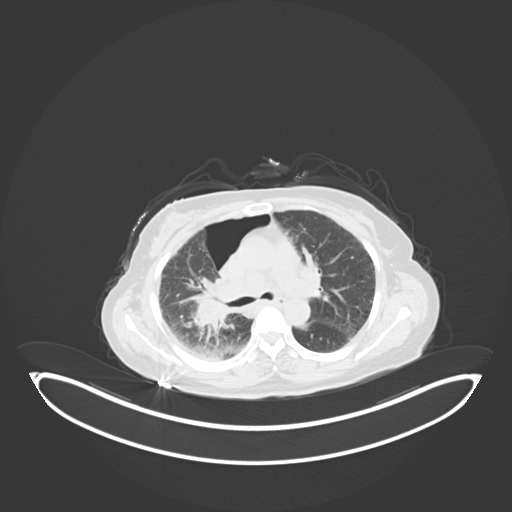
Chest CT, one axial slice. Position 36 of 69 along the scan axis. Reconstruction kernel B30f. 120 kVp. Lung window (W 1500 / L -600 HU). 3 mm slice thickness. 512 × 512 image matrix, field of view 500 × 500 mm. Female patient, age 64 years. Case-level facts recorded for this patient, not image findings: clinical TNM (as recorded): T3 N3 M0.
Outlined on this slice (rectangle marked by the reading radiologist):
- lung tumour (recorded histology: squamous cell carcinoma): bounding box [x1, y1, x2, y2] px = [183, 281, 236, 338]